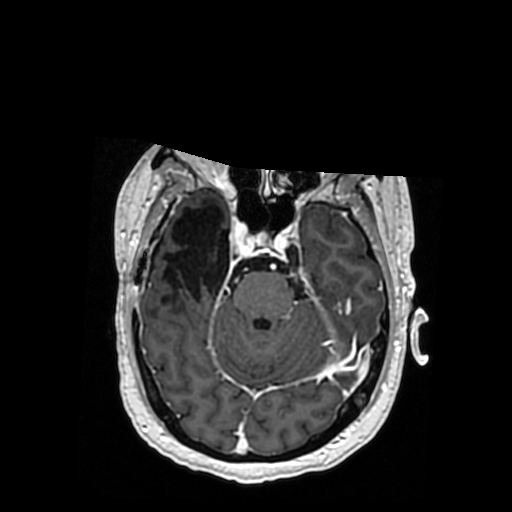
Brain MRI from a brain-tumour surgery series, one axial slice. Position 236 of 364 along the scan axis. T1-weighted post-contrast. 512 × 512 image matrix. From the clinical record (not read from this slice): histopathology: Oligodendroglioma; WHO grade: 3; IDH mutation: yes; tumour location: Right Posterior Temporal Inferior Parietal.
Annotated regions visible in this slice (manually delineated by an expert):
- previous resection cavity: bounding box [x1, y1, x2, y2] px = [161, 206, 229, 304]